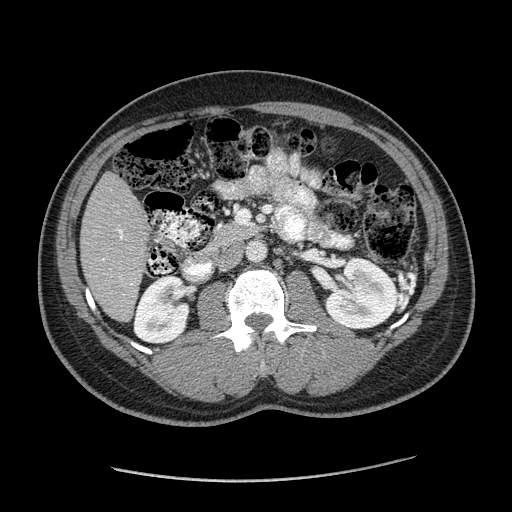
Contrast-enhanced abdominal CT (liver protocol), one axial slice; position 59 of 182 along the scan axis; 120 kVp; soft-tissue window (W 400 / L 40 HU); 512 × 512 image matrix, field of view 400 × 400 mm. From the clinical record (not read from this slice): diagnosis: hepatocellular carcinoma (patient treated with transarterial chemoembolisation; whether this scan precedes or follows treatment is not stated here); TNM stage (as recorded): Stage-I; Child-Pugh class: A.
Annotated regions visible in this slice (semi-automatically segmented with operator editing):
- liver parenchyma outside the tumour (the mass and vessels are separate outlines, so this box may not span the whole liver): bounding box <80,172,148,320> (left, top, right, bottom; pixels)
- liver vessels: <102,229,123,260>